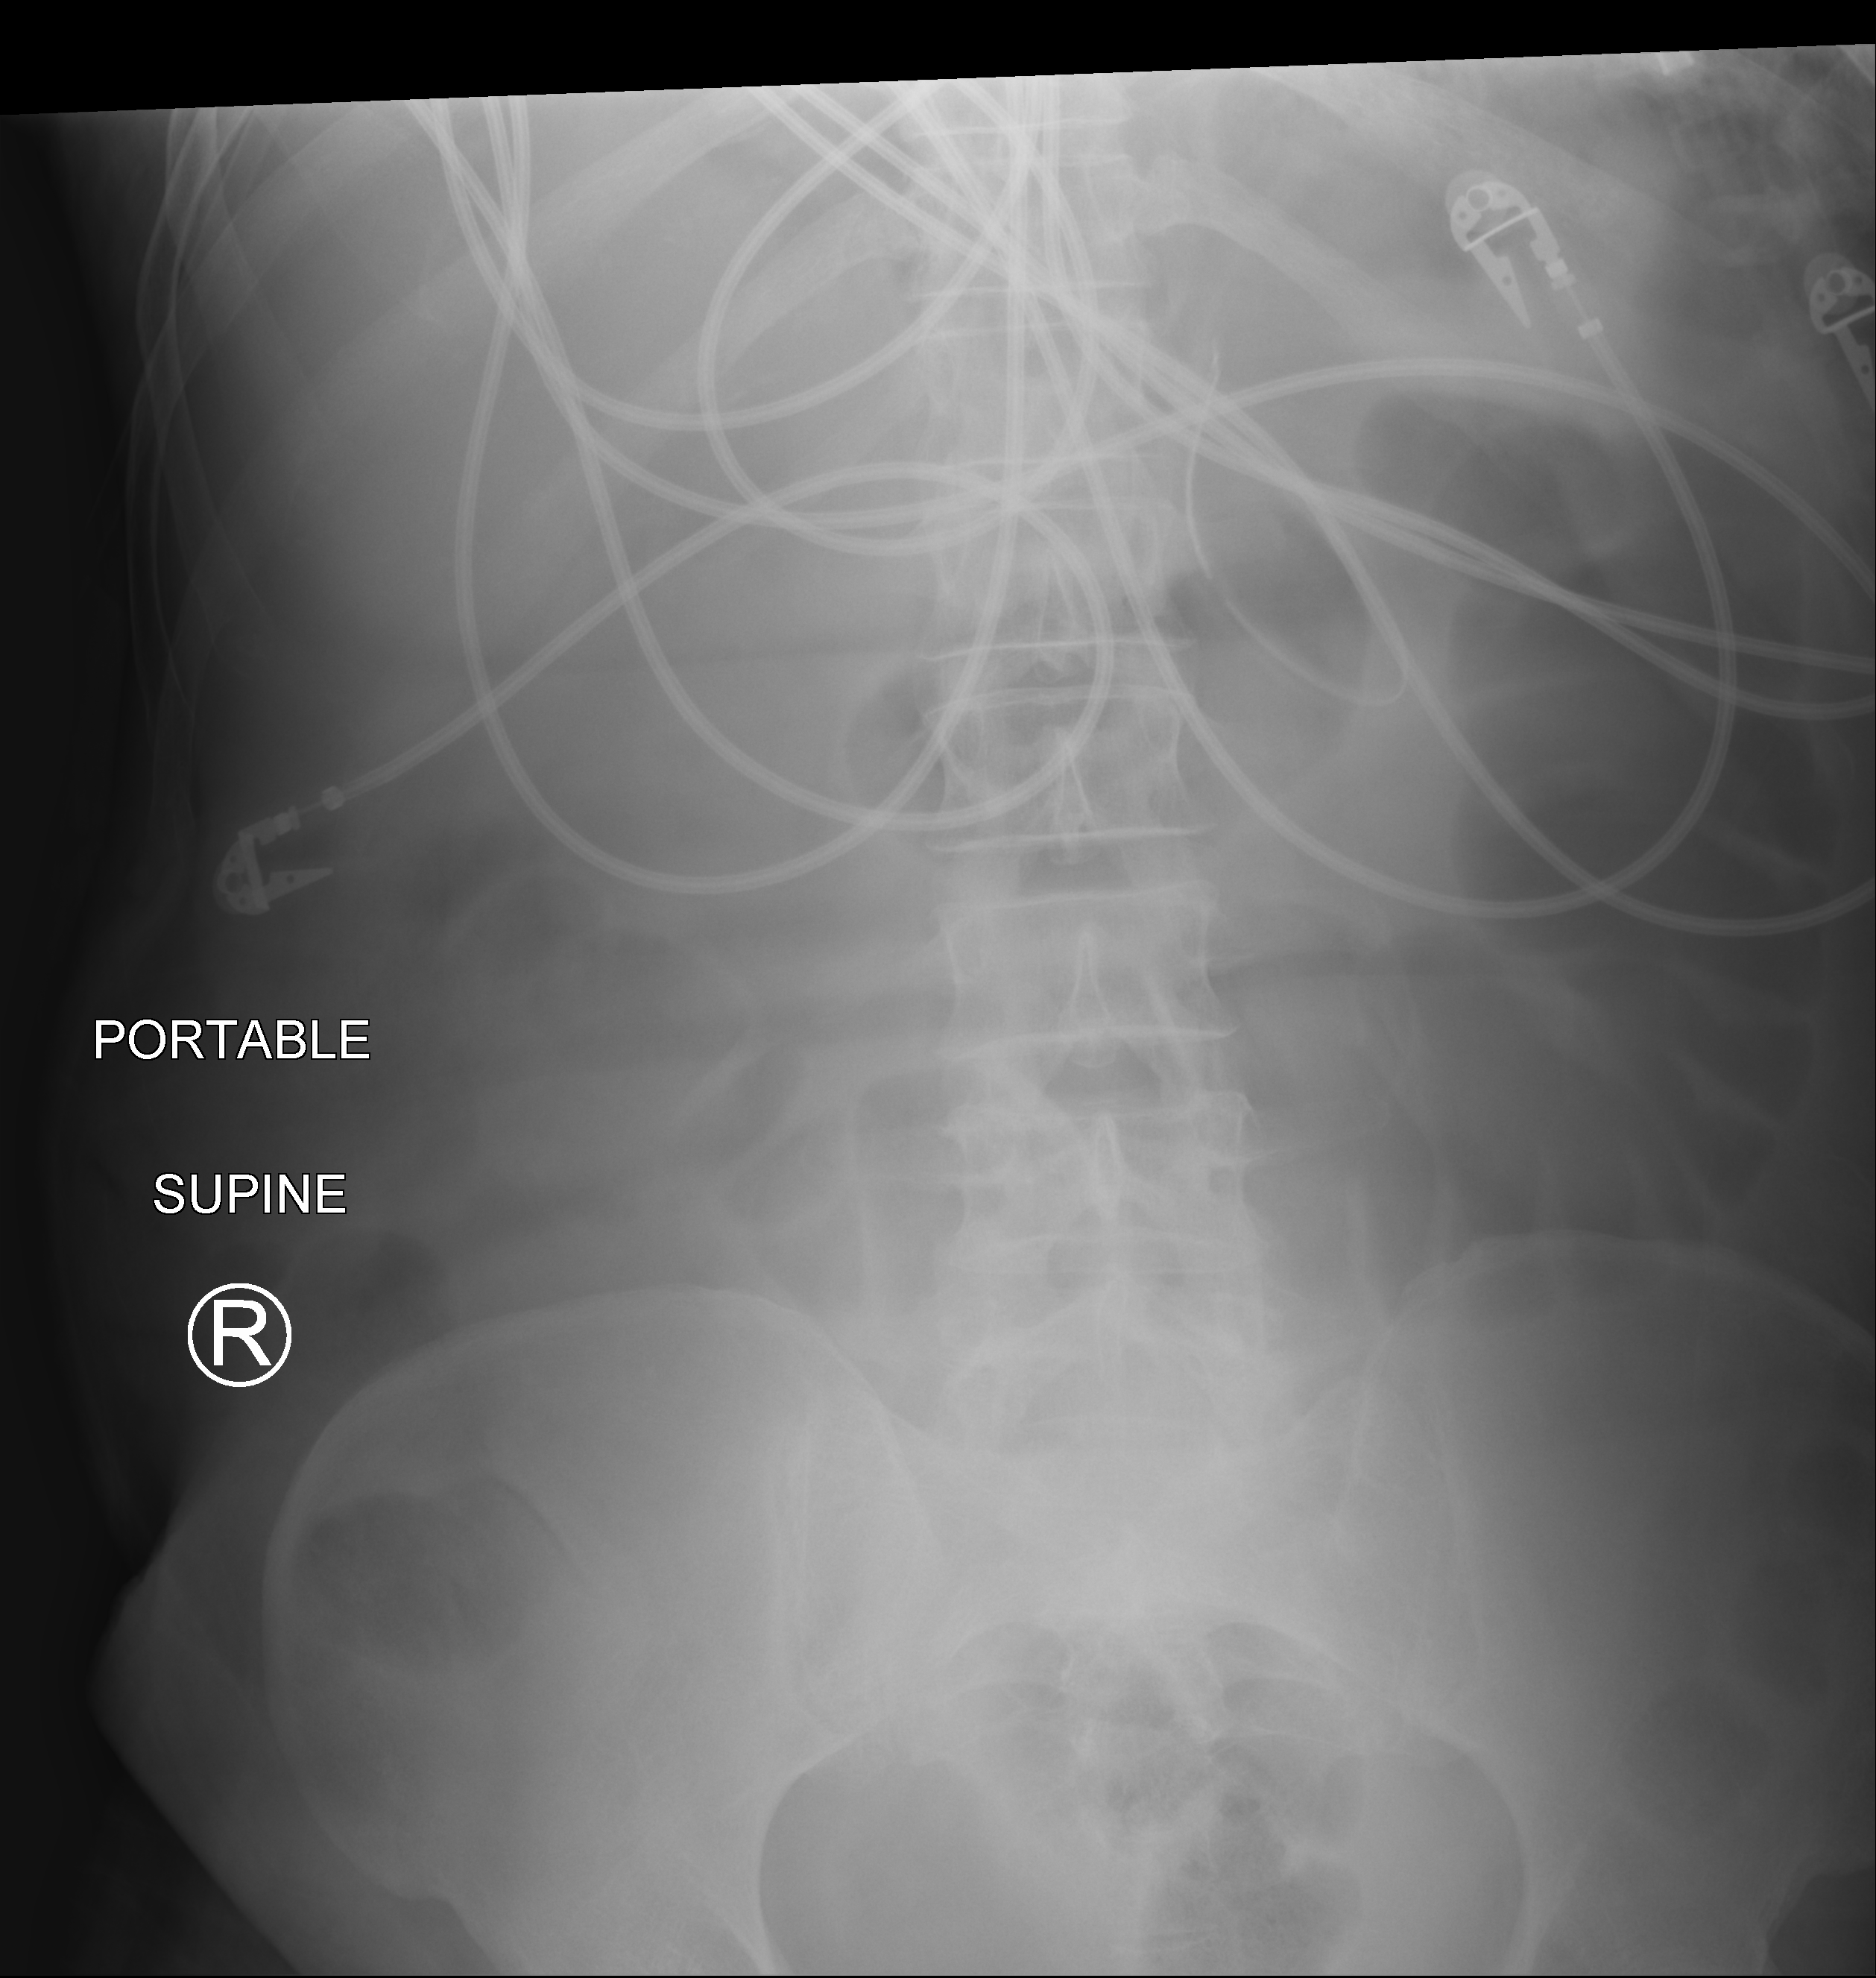
Bedside abdomen radiograph (computed radiography), anteroposterior (AP) projection. Patient hospitalised with COVID-19; male, aged 60–74 years.
From the hospital-stay record, not from the radiograph (when in the stay this image was taken is not recorded): mechanically ventilated during this hospital stay: yes; admitted to intensive care during this hospital stay: yes.